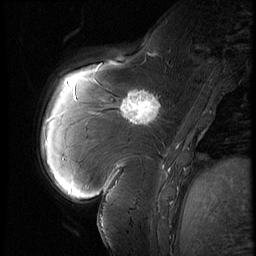
Breast MRI (dynamic contrast-enhanced), one sagittal slice. Slice 19 of 60 in the series (ordered by position). 3 images stored at this slice position (order not interpretable as contrast timing). 1.5 T. TE 4.2 ms, TR 9 ms. 256 × 256 image matrix, field of view 180 × 180 mm. Female patient, age 57 years. Case-level facts recorded for this patient, not image findings: setting: breast cancer imaged before/during neoadjuvant chemotherapy; receptor status: triple-negative.
Annotated regions visible in this slice (semi-automatic segmentation, software-assisted and operator-edited):
- analysis volume of interest (the breast-tissue region the enhancement analysis was run in; not a lesion): bounding box (x1, y1, x2, y2) in pixels: (114, 83, 170, 131)
- tumour enhancement mask (voxels above the 140 % enhancement threshold inside the analysis volume of interest): (118, 92, 160, 125)